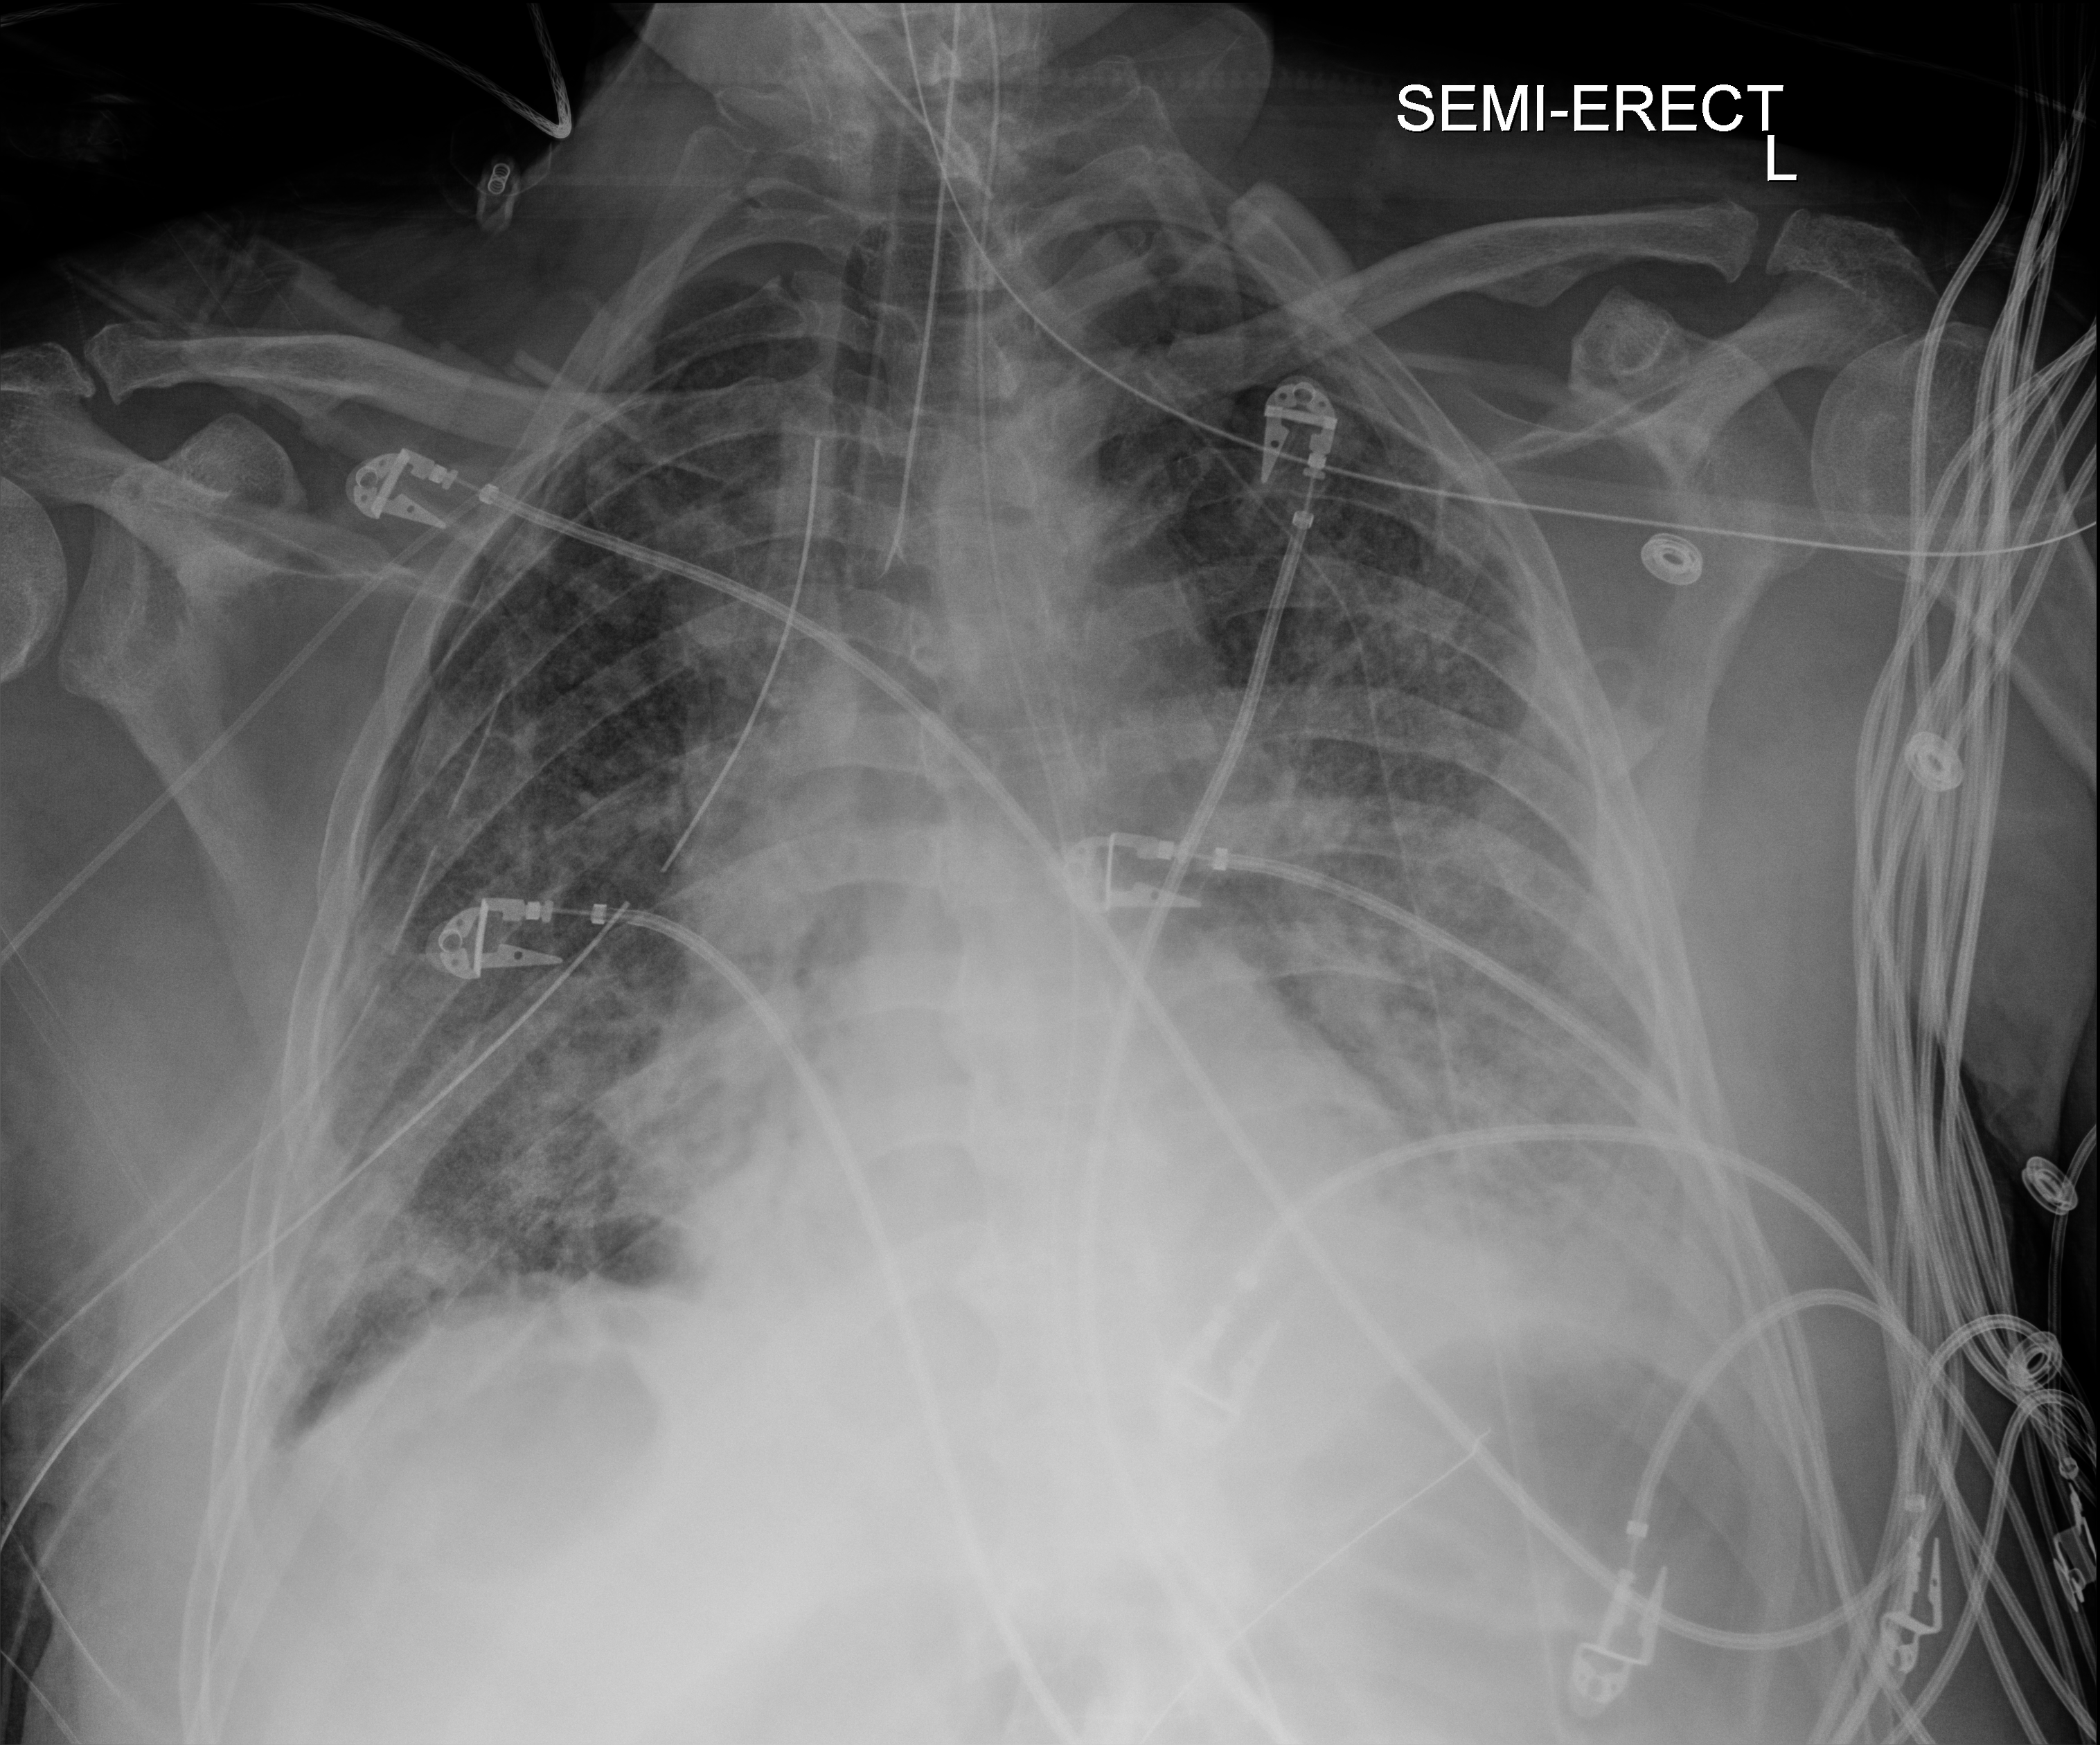
Chest radiograph (digital radiography), anteroposterior (AP) projection. Patient hospitalised with COVID-19; male, aged 60–74 years.
Admission-level facts for this patient (not findings on this image; timing relative to this image not recorded): other chronic lung disease (admission record): no; admitted to intensive care during this hospital stay: yes; mechanically ventilated during this hospital stay: yes.